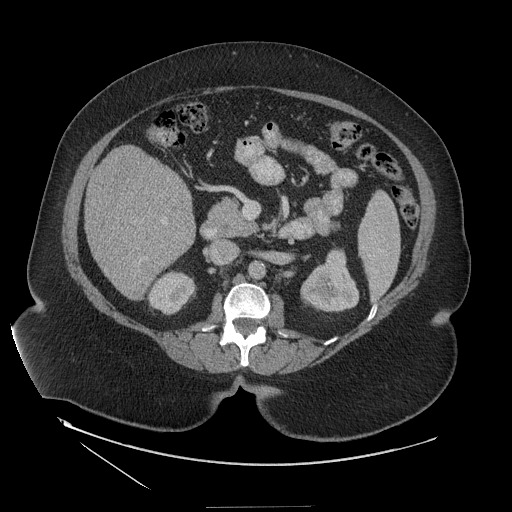
Contrast-enhanced abdominal CT (liver protocol), one axial slice. Slice 54 of 127 in the series (ordered by position). Reconstruction kernel STANDARD. 140 kVp. Soft-tissue window (W 400 / L 40 HU). 512 × 512 image matrix. From the clinical record (not read from this slice): diagnosis: hepatocellular carcinoma (patient treated with transarterial chemoembolisation; whether this scan precedes or follows treatment is not stated here); TNM stage (as recorded): Stage-II; Child-Pugh class: A; tumour differentiation: well differentiated.
Annotated regions visible in this slice (semi-automatically segmented with operator editing):
- liver parenchyma outside the tumour (the mass and vessels are separate outlines, so this box may not span the whole liver): bounding box <84,146,196,299> (left, top, right, bottom; pixels)